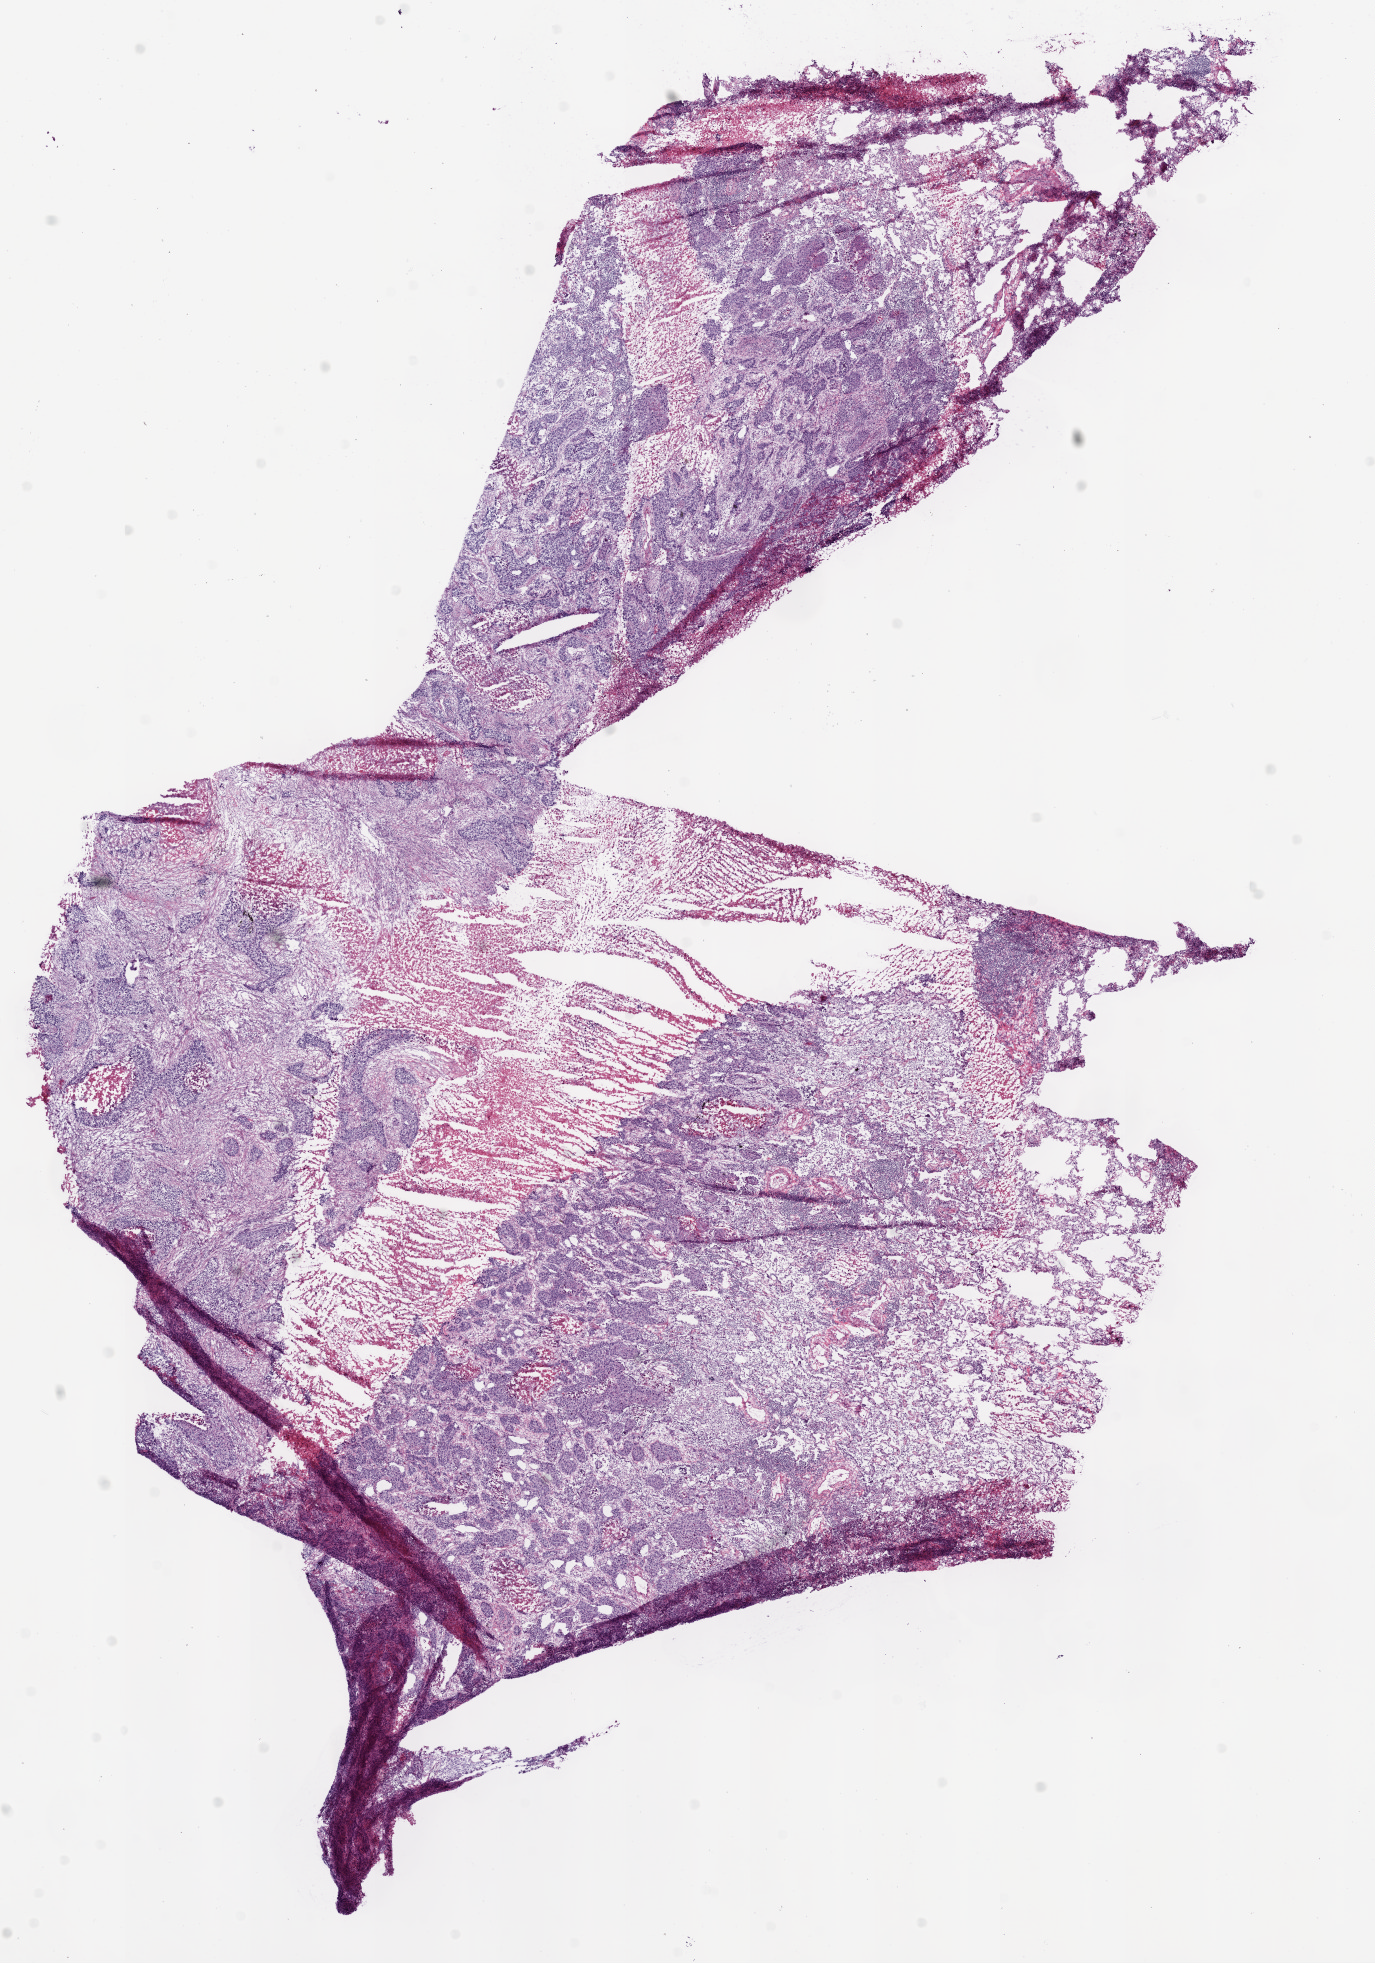
Digitized H&E tissue section (whole slide), low-resolution overview of the scanned area, about 11.0 x 15.8 mm (acquisition: 20x scan), frozen section from the bottom of the tissue portion, sample: primary tumour, lung. Male patient; age at initial diagnosis 70 years. Pathologist review of this section (percent, as recorded): tumour cells 47%, tumour nuclei 60%, normal cells 15%, stromal cells 8%, necrosis 30%. Infiltration values recorded for this section: lymphocyte infiltration 30%, monocyte infiltration 1%, neutrophil infiltration 0%.
Histologic diagnosis: Squamous cell carcinoma, NOS (upper lobe, lung). AJCC pathologic stage: IIIB (5th edition). Laterality: right.